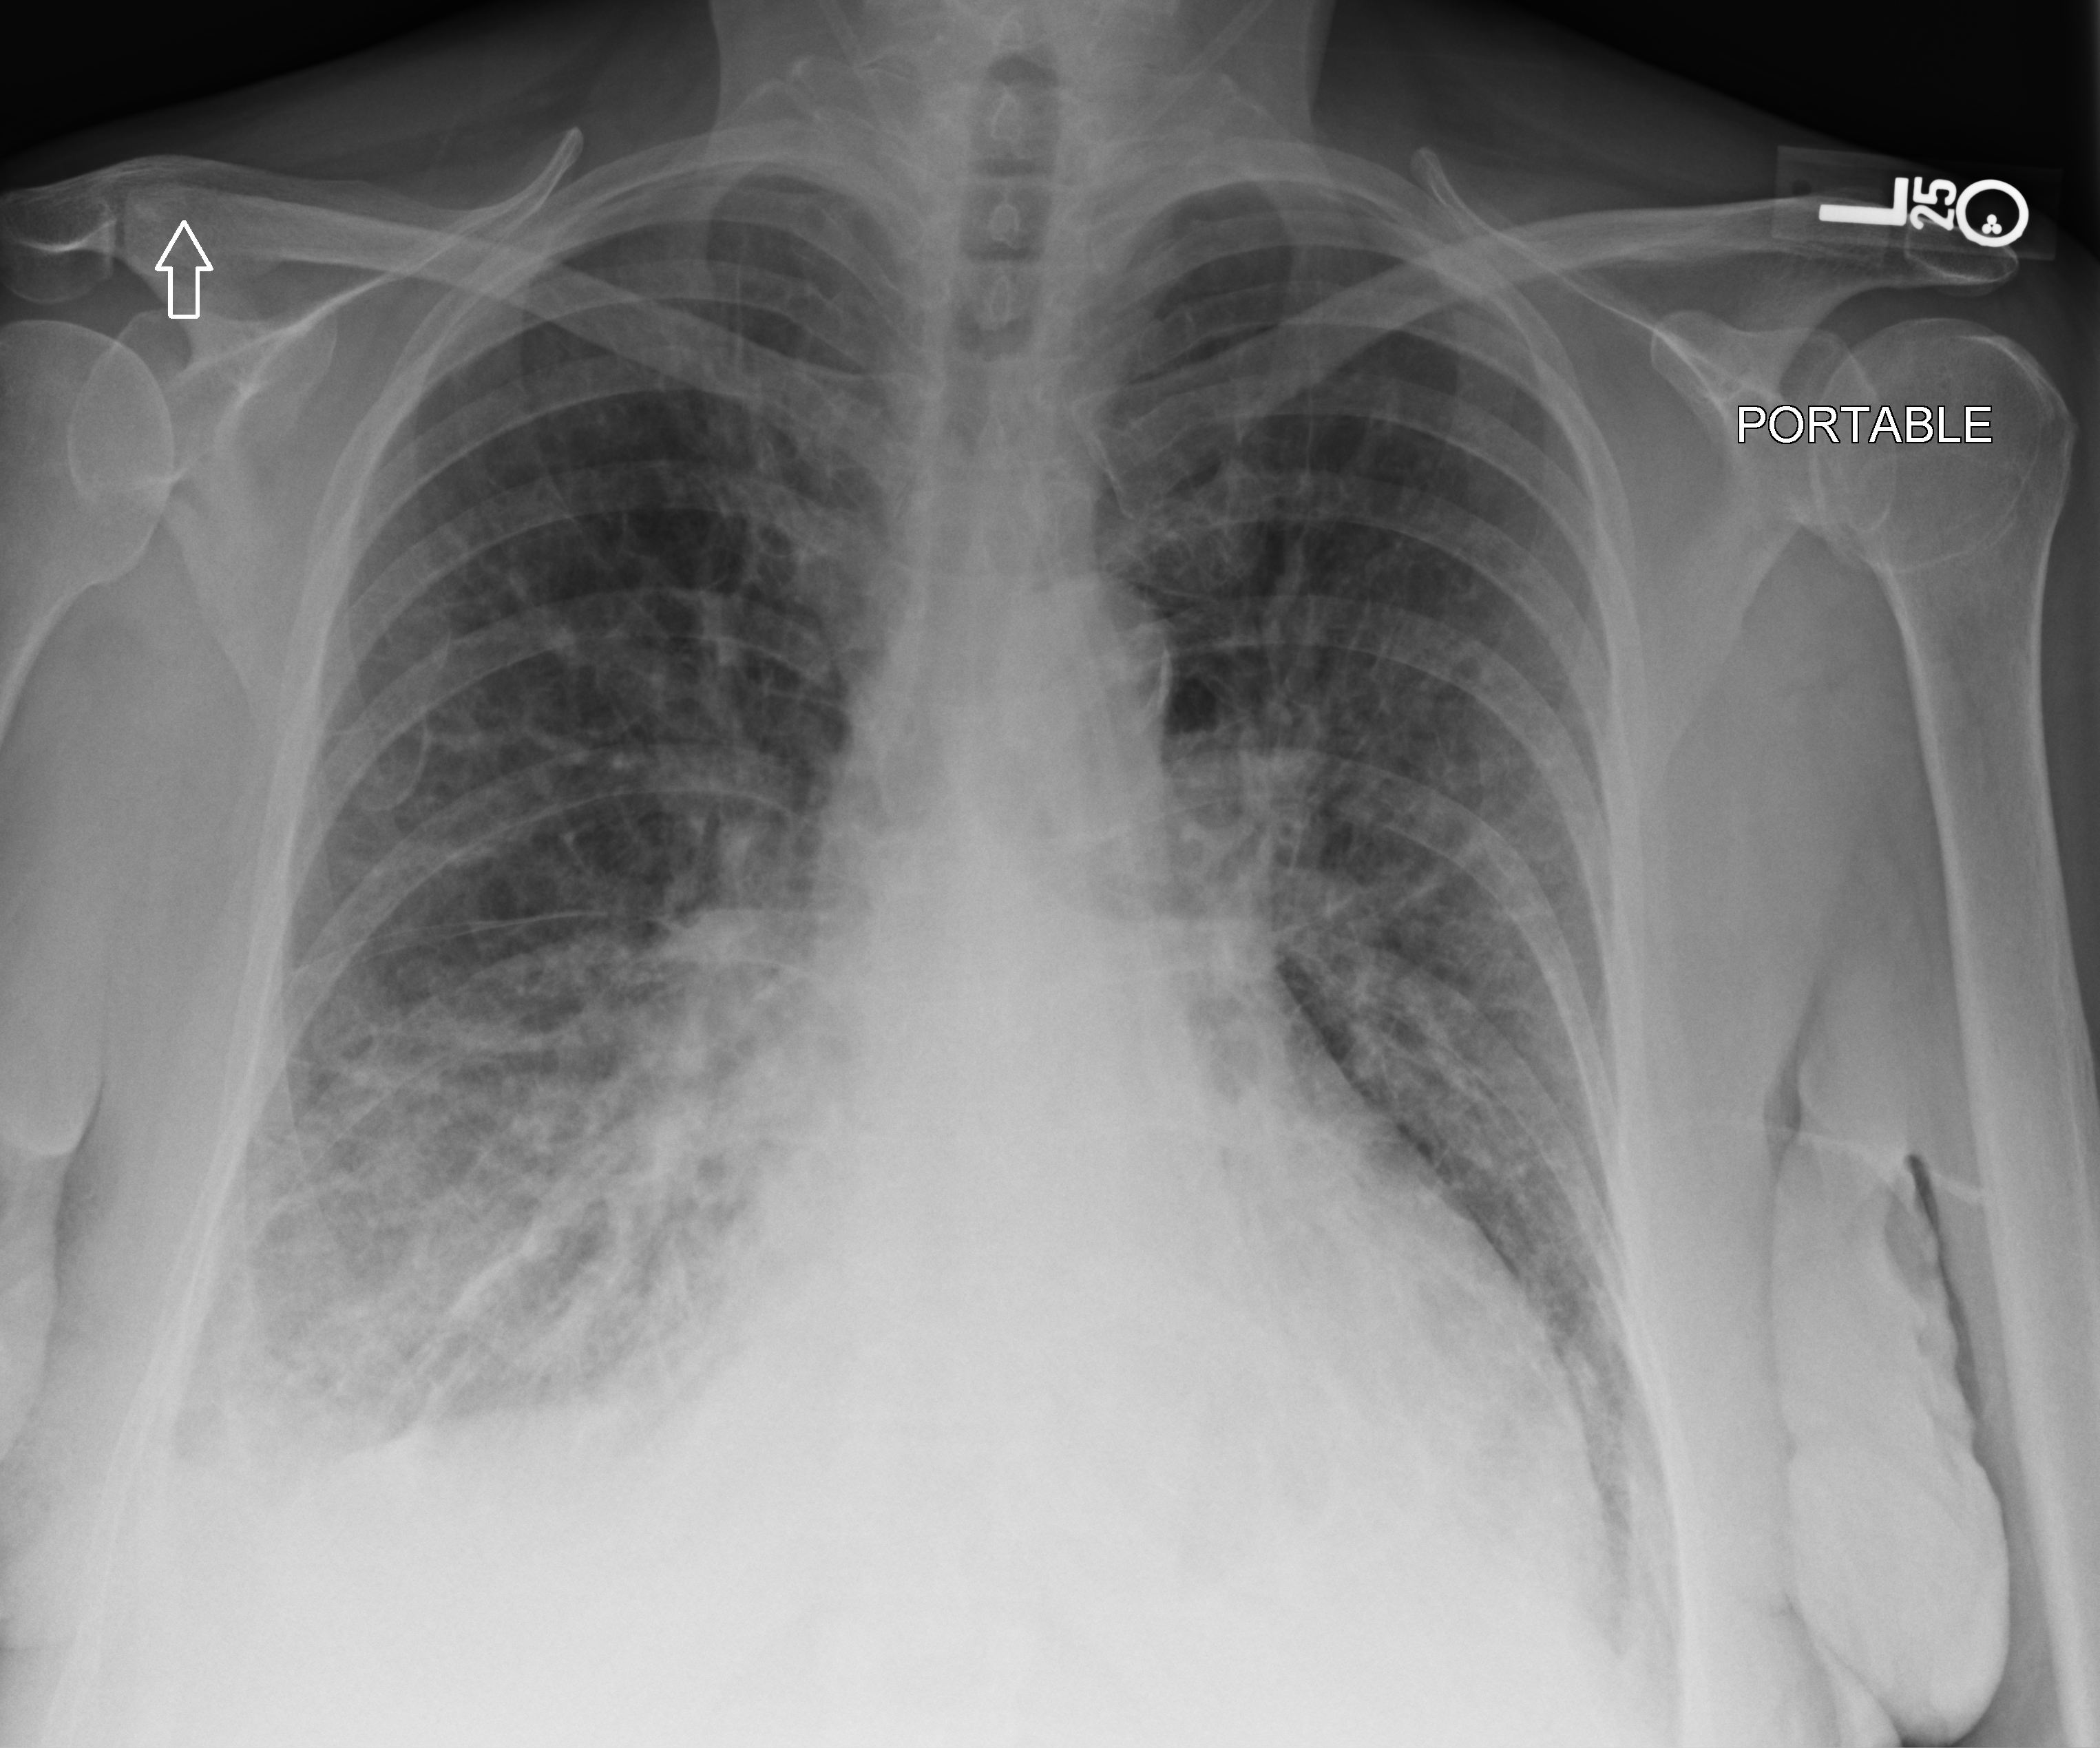
Chest X-ray (portable). Female patient hospitalised with COVID-19, age 18–59 years.
Admission-level facts for this patient (not findings on this image; timing relative to this image not recorded):
- admitted to intensive care during this hospital stay: no